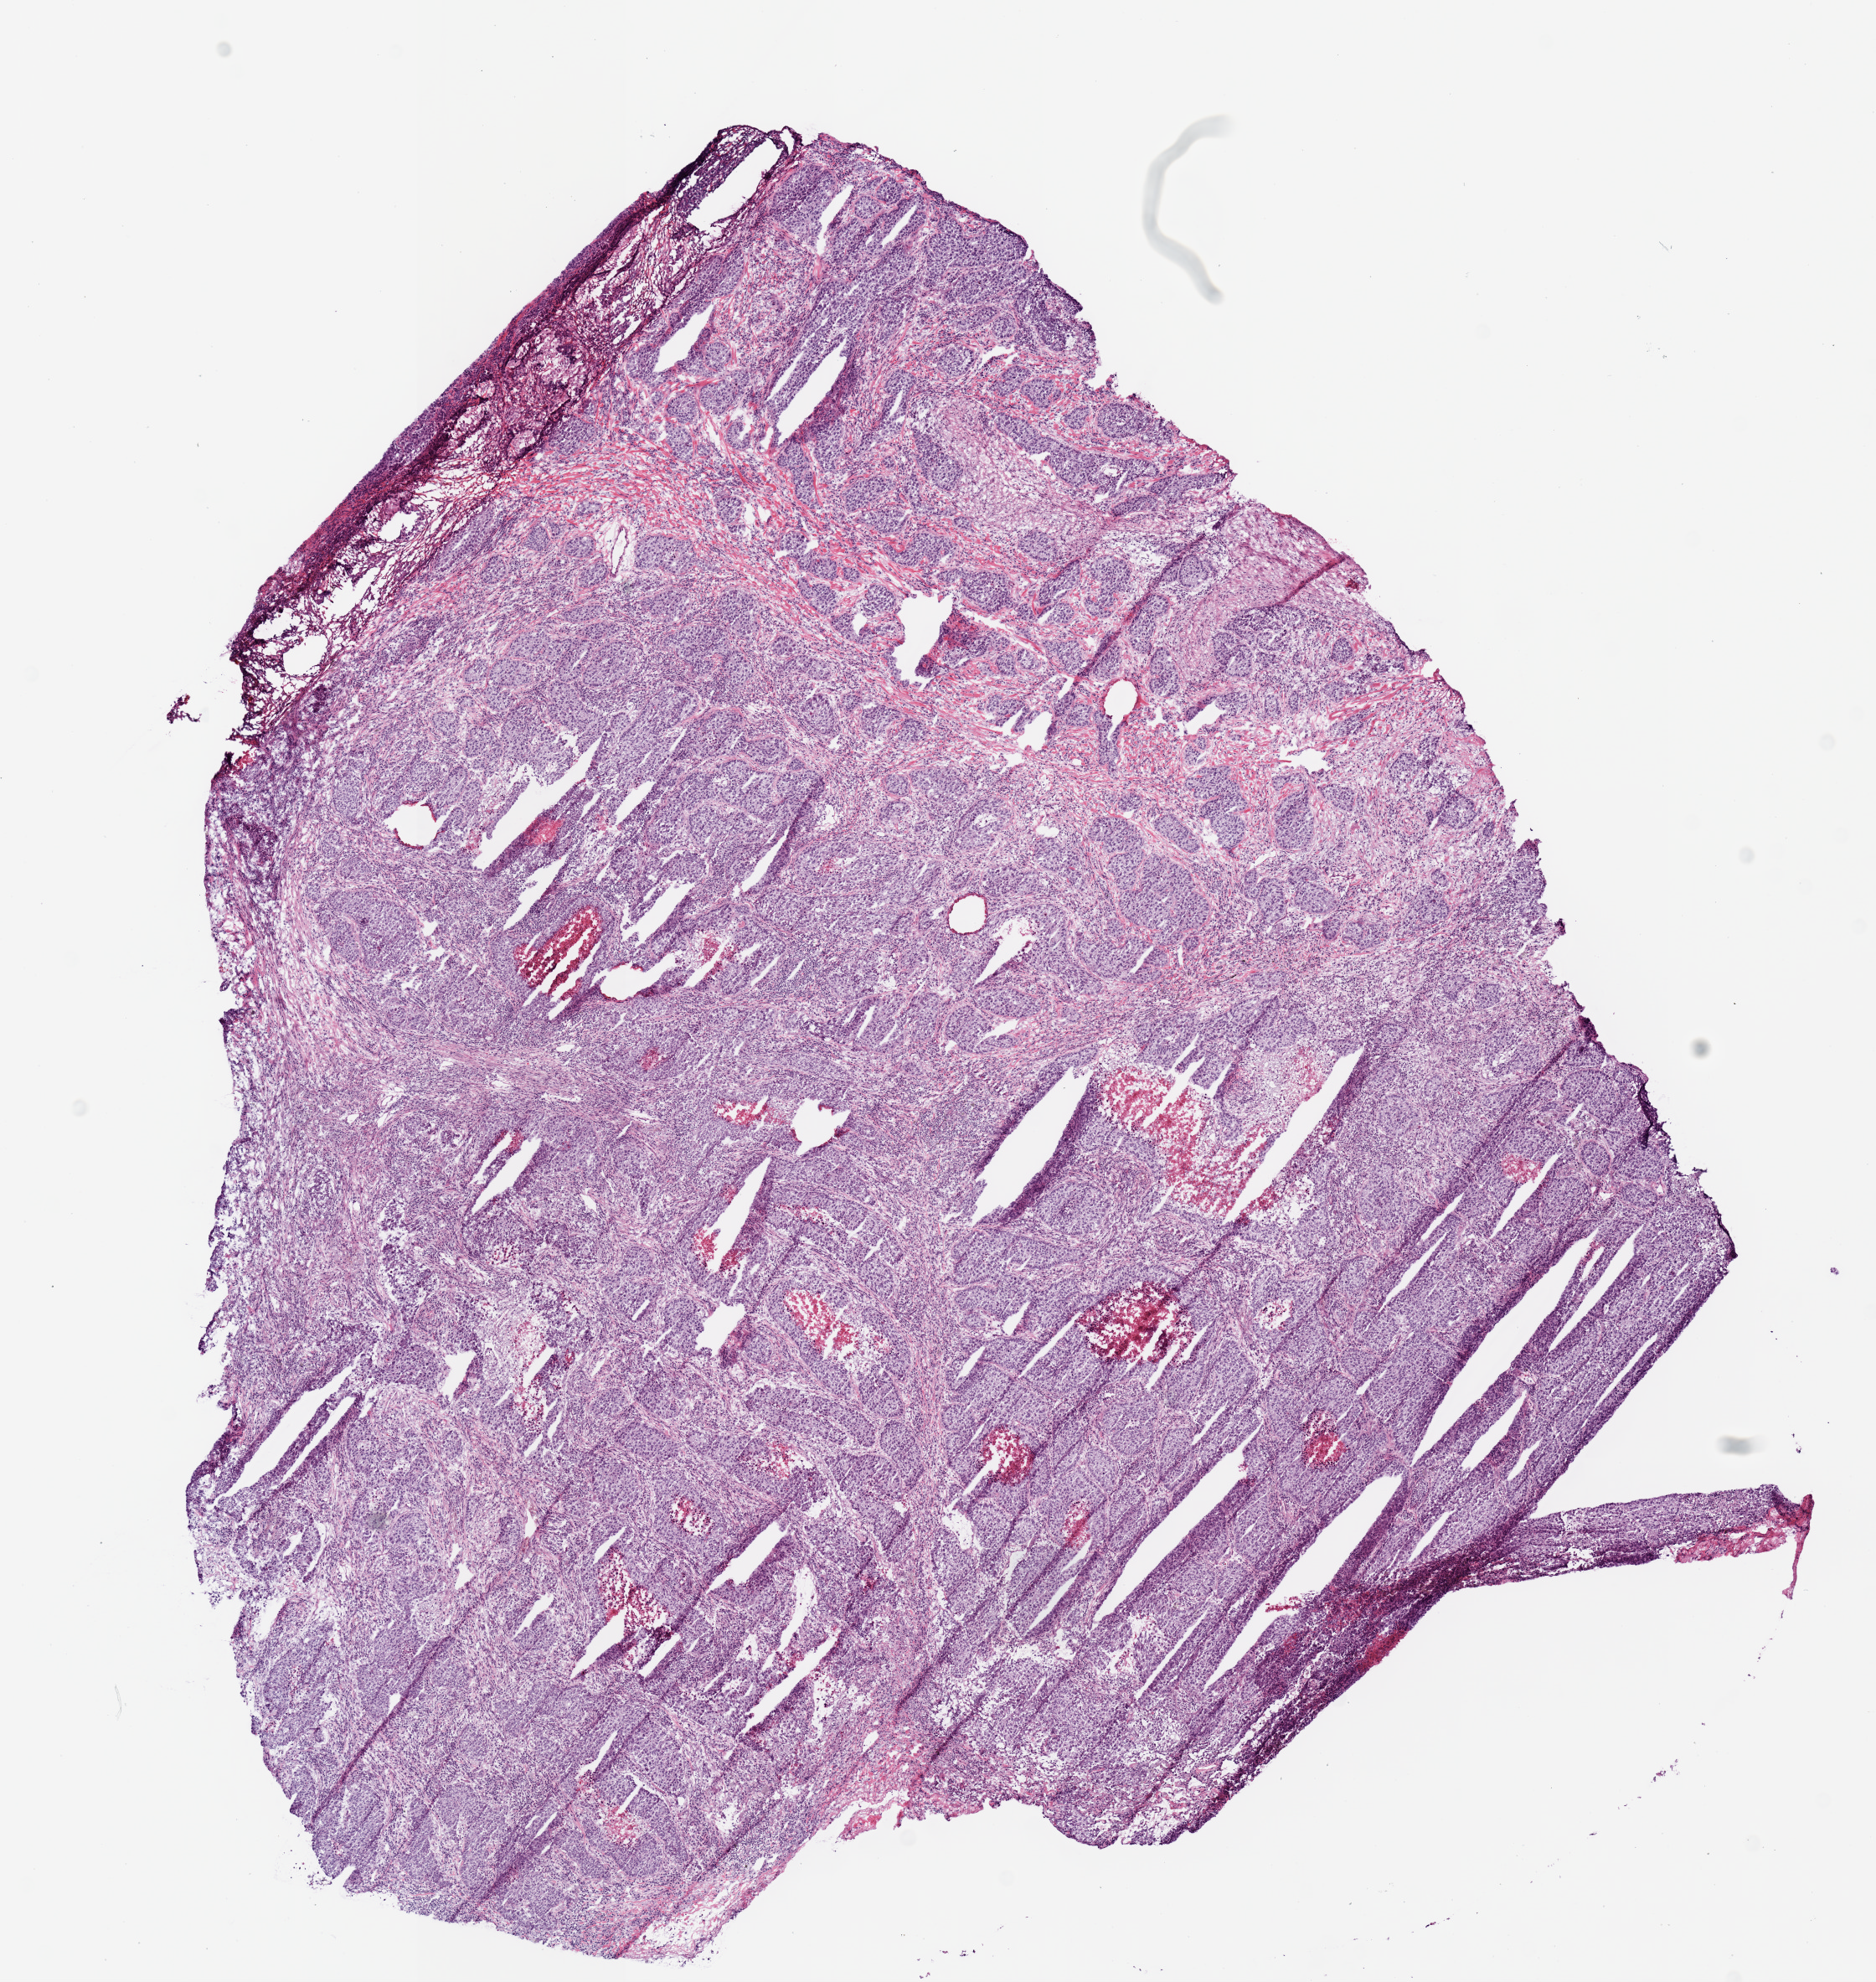
H&E whole-slide image, a low-resolution overview of the entire scanned area, about 8.9 x 9.4 mm (from a 20x scan), frozen section from the top of the tissue portion, lung, primary tumour sample. Male, age 60 years at initial diagnosis. Slide review estimates, as recorded: tumour cells 95%, tumour nuclei 80%, normal cells 0%, stromal cells 0%, necrosis 5%. Infiltration values recorded for this section: lymphocyte infiltration 15%, monocyte infiltration 0%, neutrophil infiltration 2%.
• AJCC pathologic stage: IV
• pathologic diagnosis: Adenocarcinoma, NOS (upper lobe, lung)